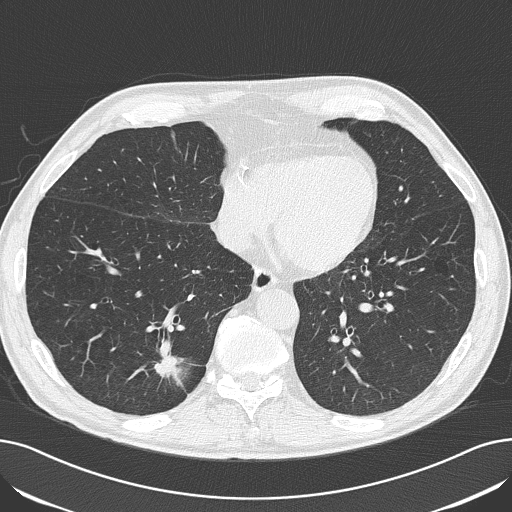
Low-dose screening chest CT, one axial slice; slice 60 of 182 in the series (ordered by position); 120 kVp; lung window (W 1500 / L -600 HU); 512 × 512 image matrix.
Structures marked on this image (manually delineated by an expert):
- lesion 1 (tumor, lower lobe of right lung): bounding box (x1, y1, x2, y2) in pixels: (154, 356, 181, 381)